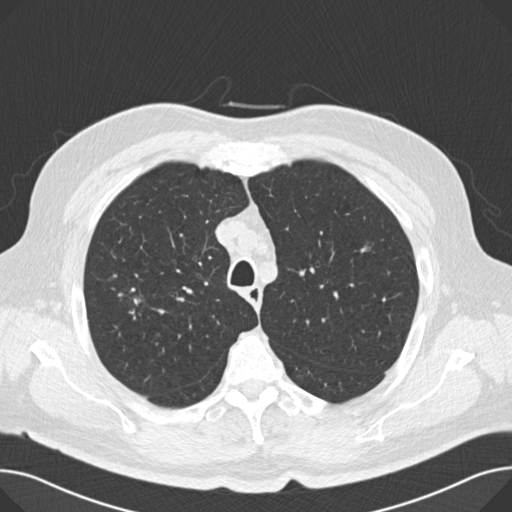
Axial slice from a low-dose chest CT screening exam. Second annual screen. Lung window (W 1500 / L -600 HU). 120 kVp. Male, age 67 years at enrolment. Current smoker at enrolment.
Expert-annotated lung lesion, bounding box [x1, y1, x2, y2] px = [126, 287, 149, 311]. No non-calcified nodule or mass ≥4 mm was recorded by the screening reader at this exam. Official screen result: negative screen, significant abnormalities not suspicious for lung cancer.